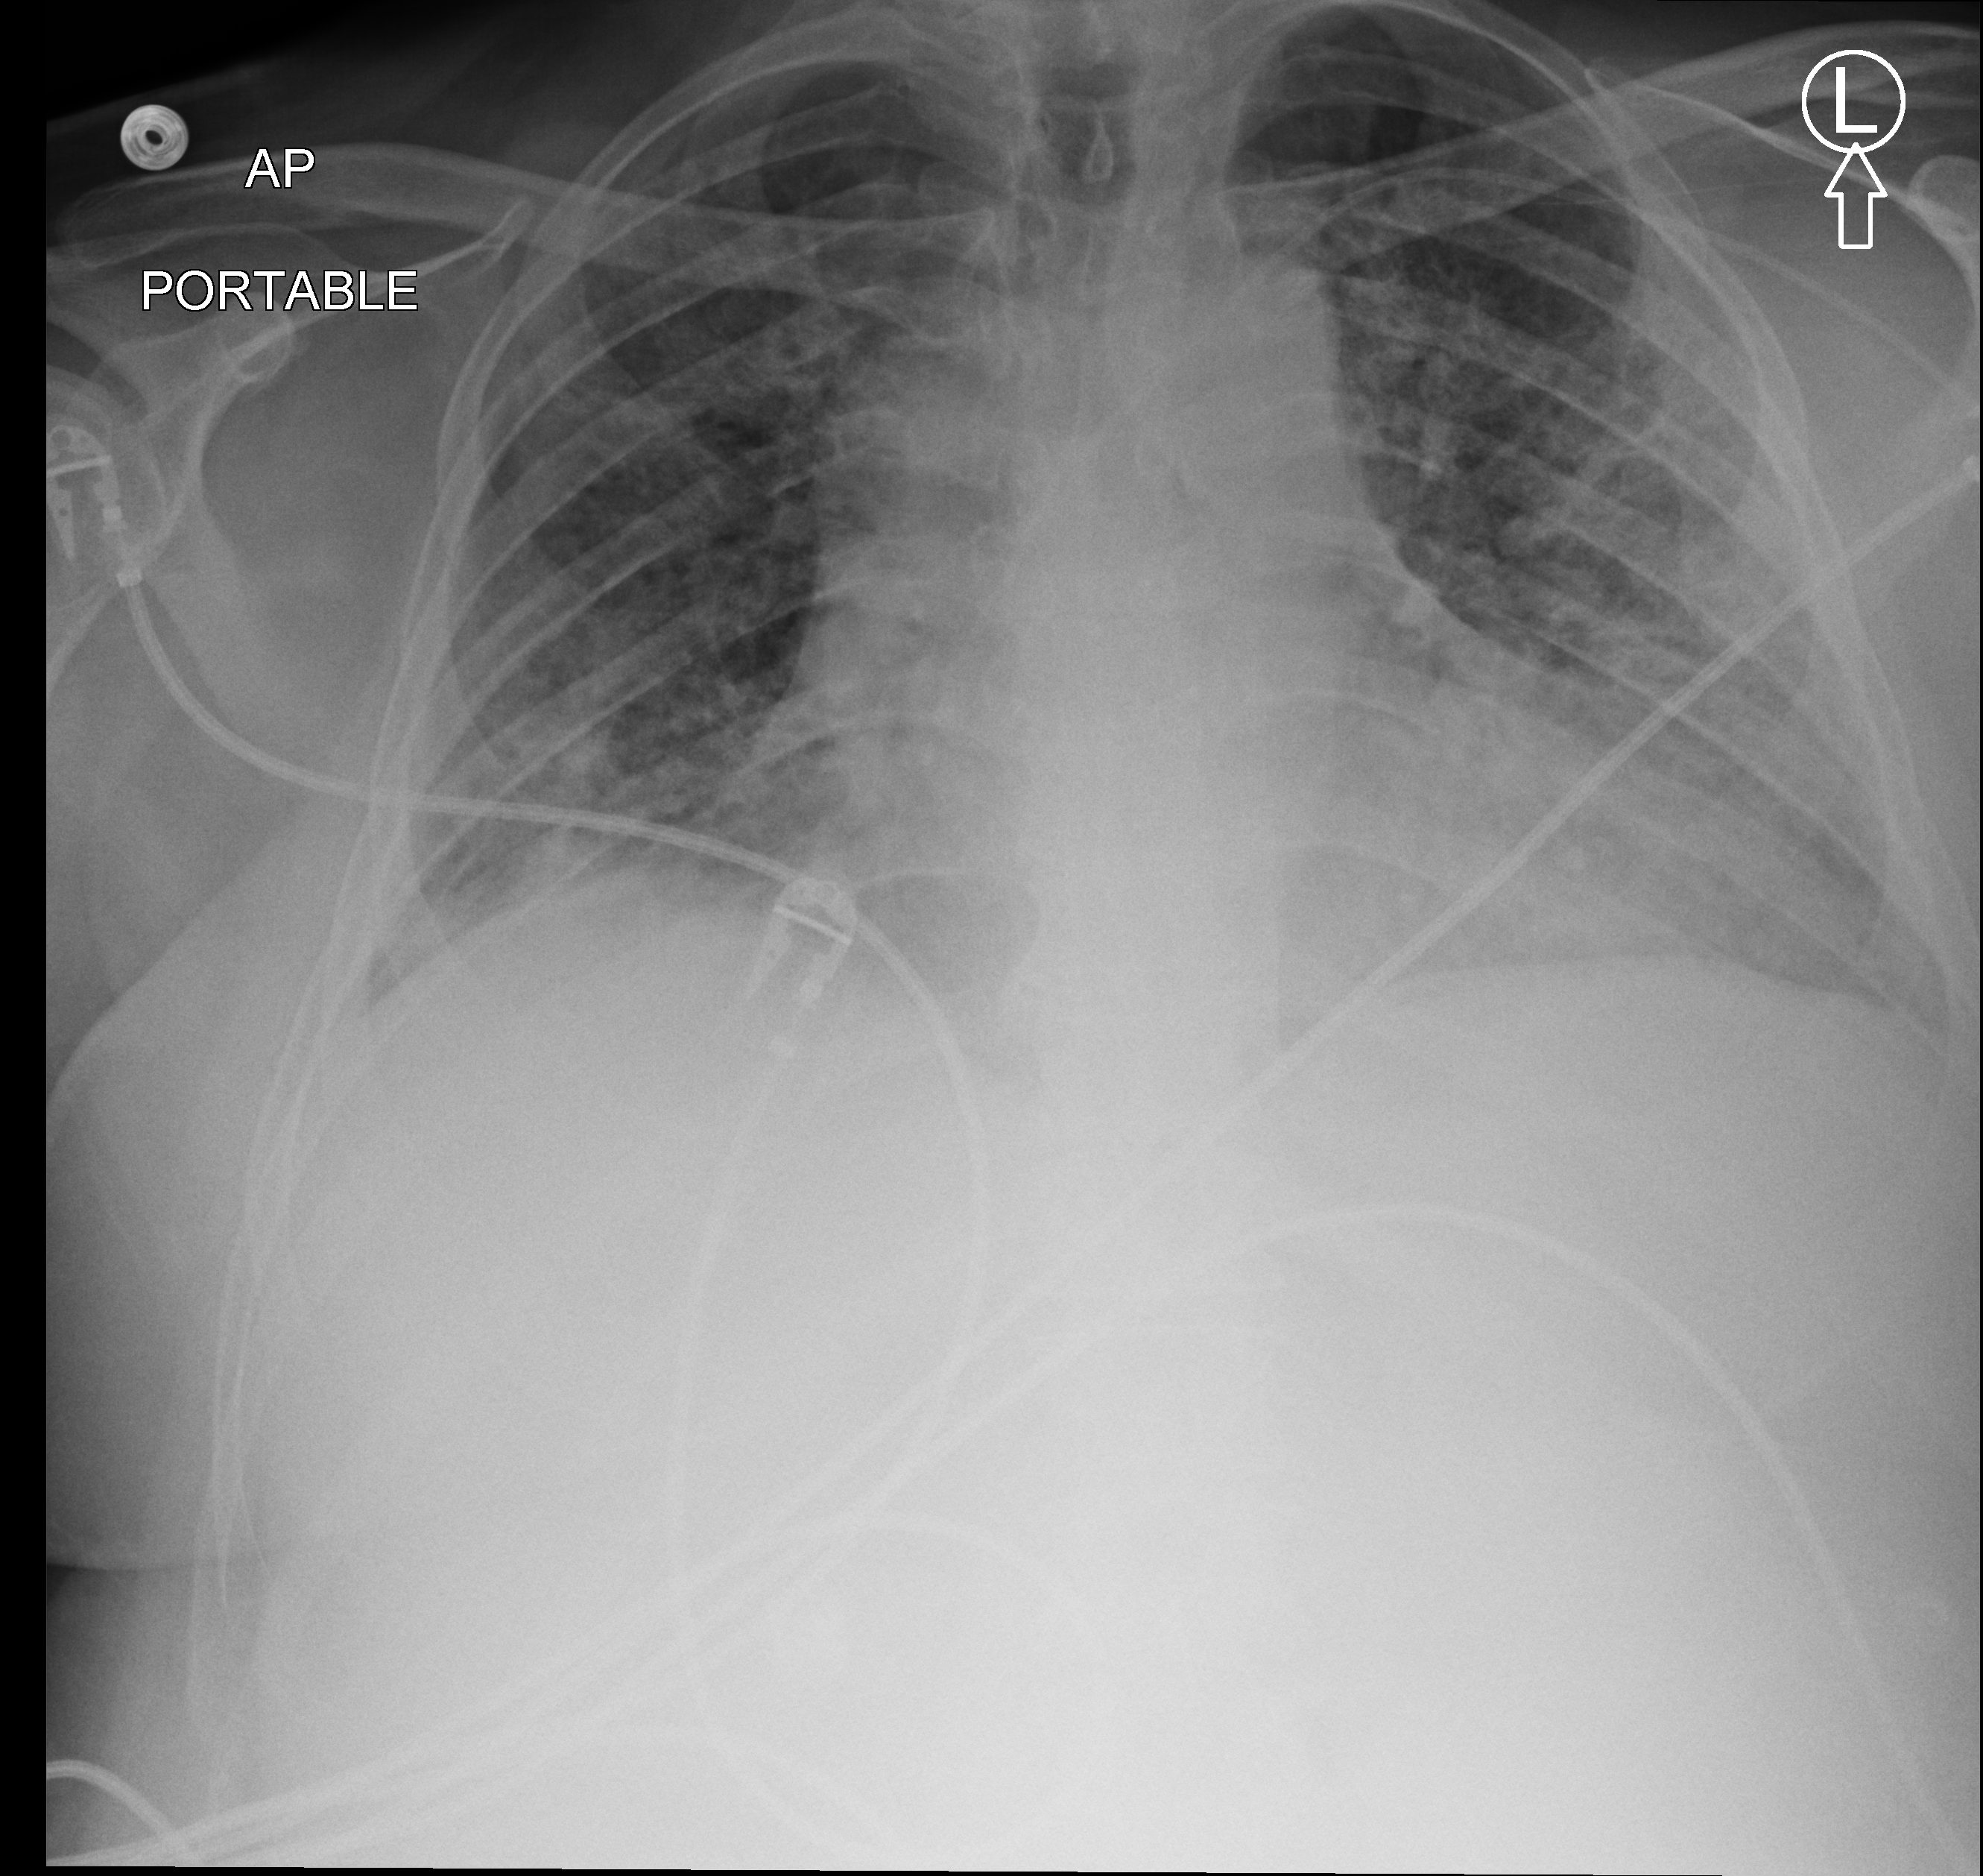
Portable chest radiograph; anteroposterior (AP) projection. Male patient hospitalised with COVID-19, age 18–59 years.
Hospital-stay facts (about this admission, not read from this image; timing relative to this image not recorded): length of hospital stay: 39 days; admitted to intensive care during this hospital stay: yes.